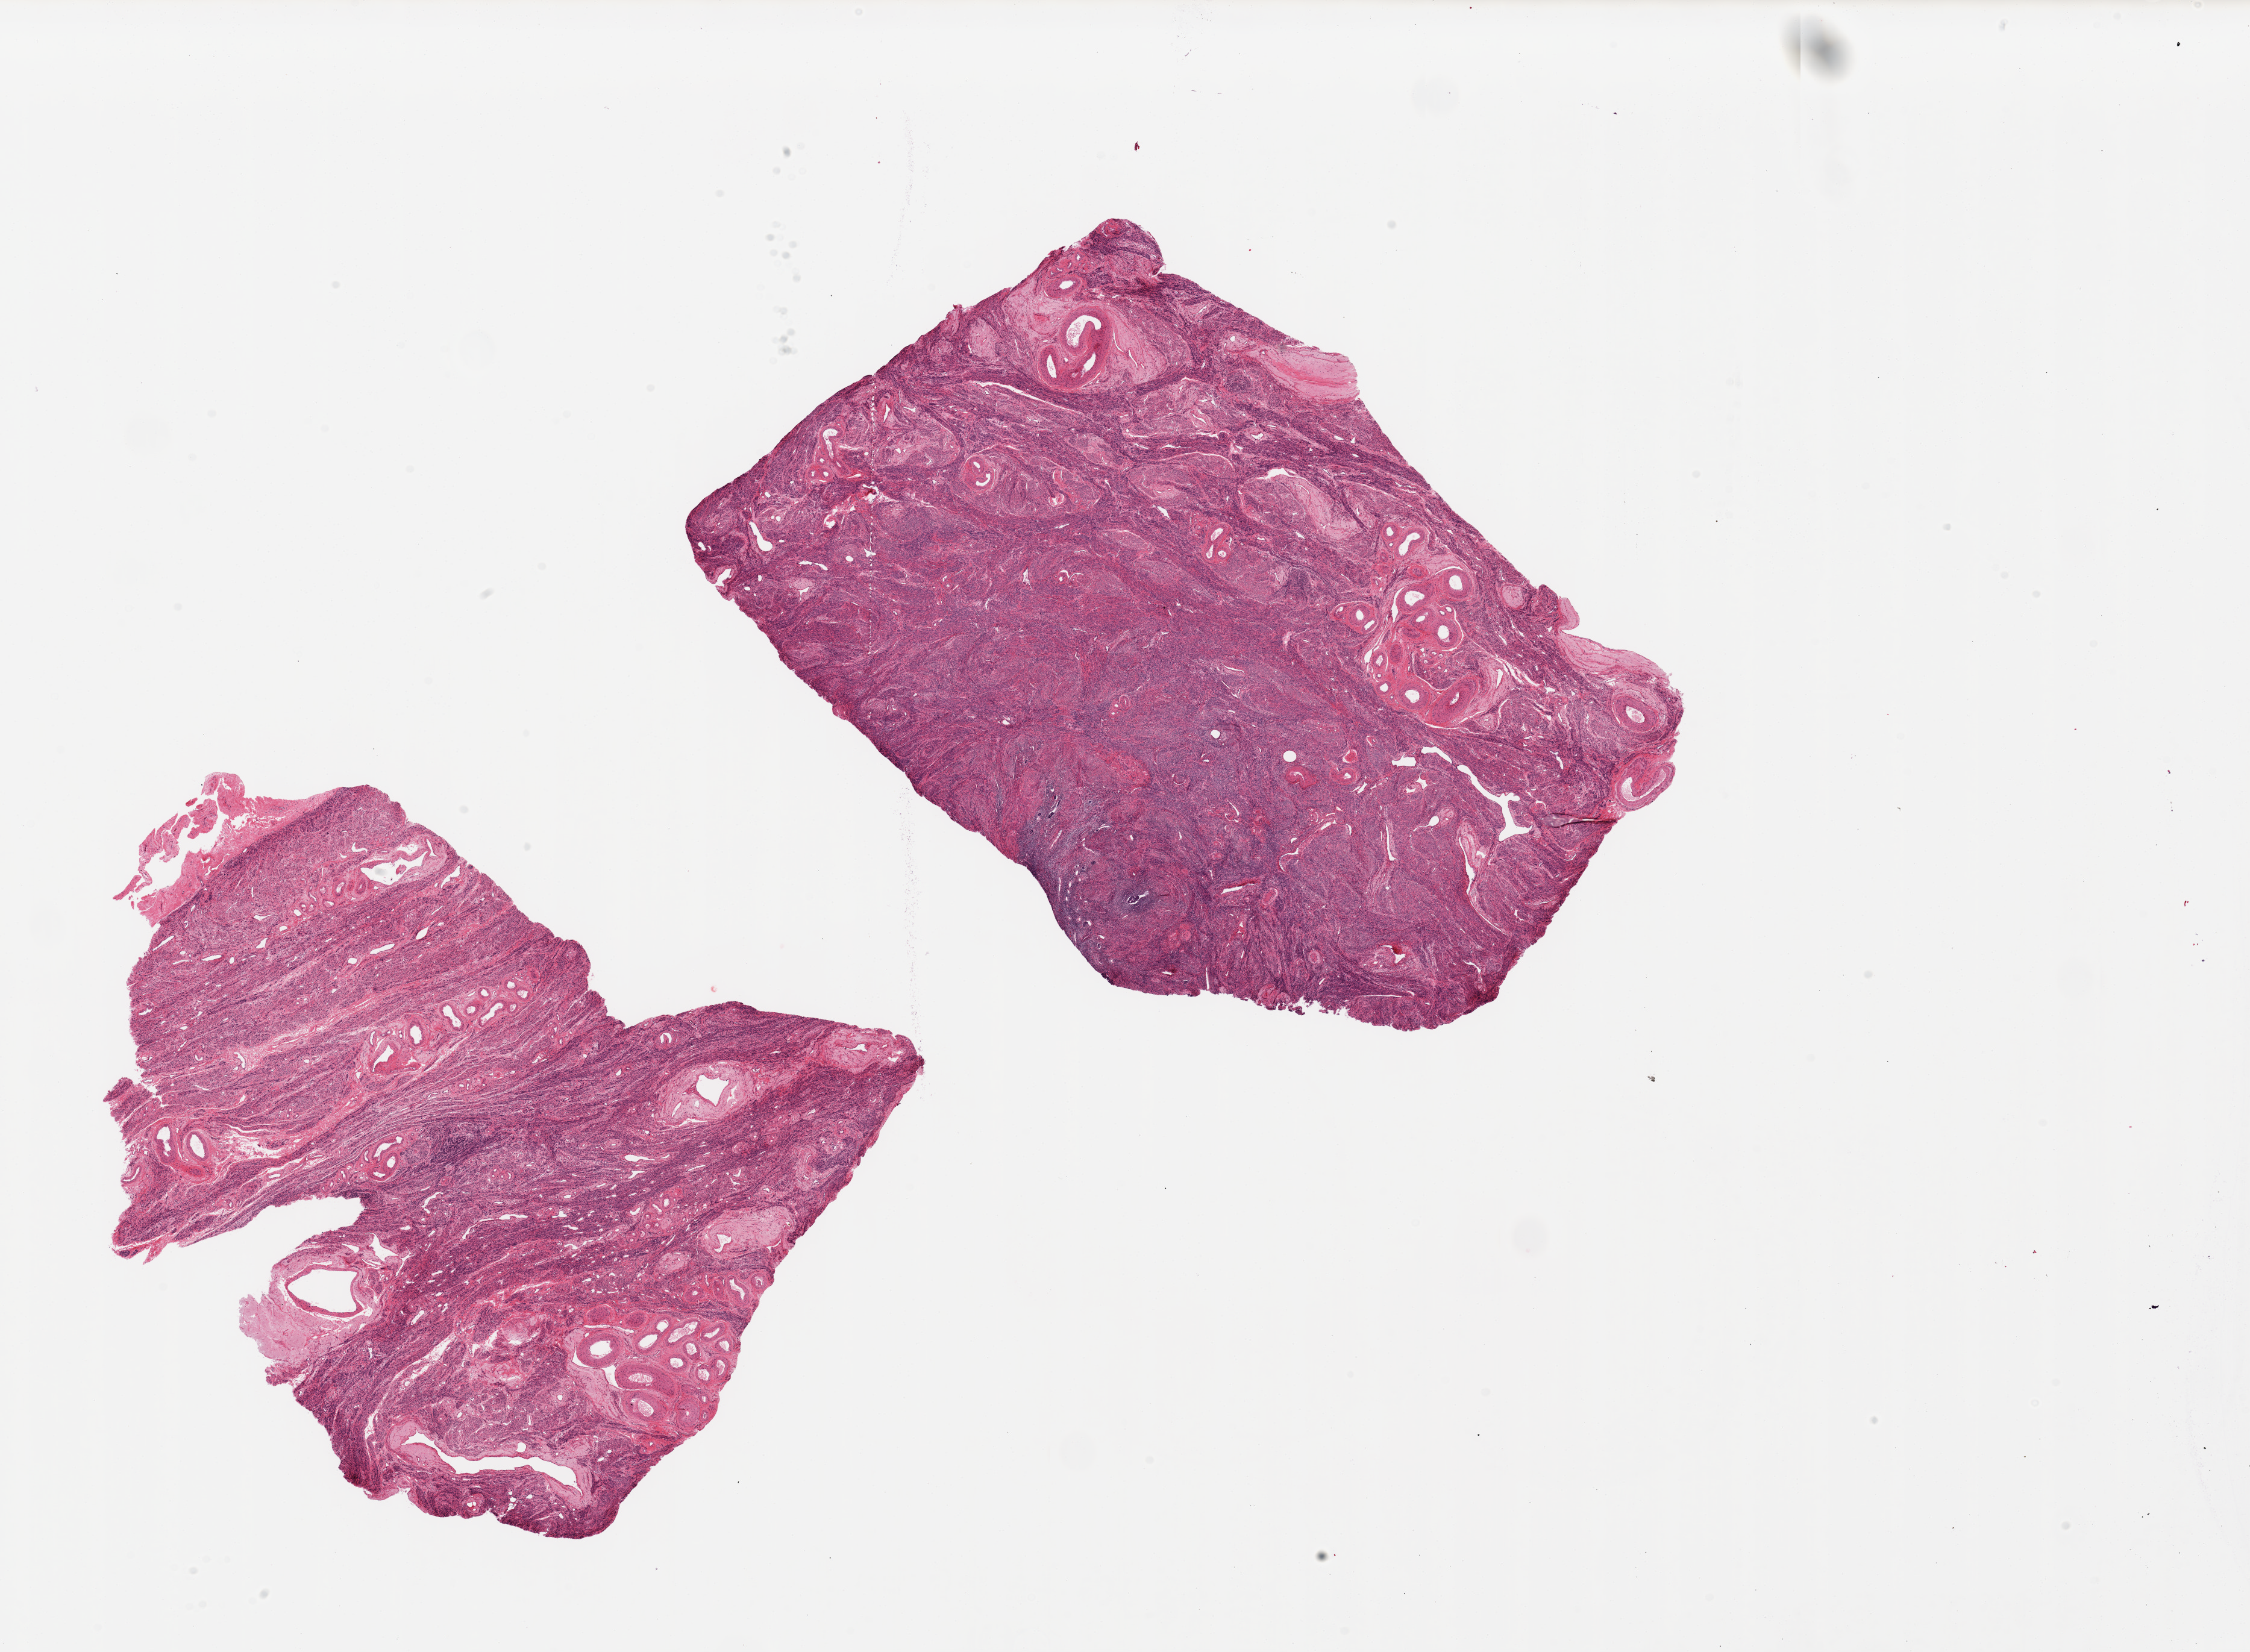
H&E whole-slide image — whole scanned area (about 29.5 x 21.7 mm, slide scanned at 20x) shown as a low-resolution overview, PAXgene-fixed paraffin-embedded (PFPE) section, target tissue: uterus, donor tissue sample.
- review note (as recorded): 2 pieces, 9x8 & 12x8mm; endometrium in one piece, not in other